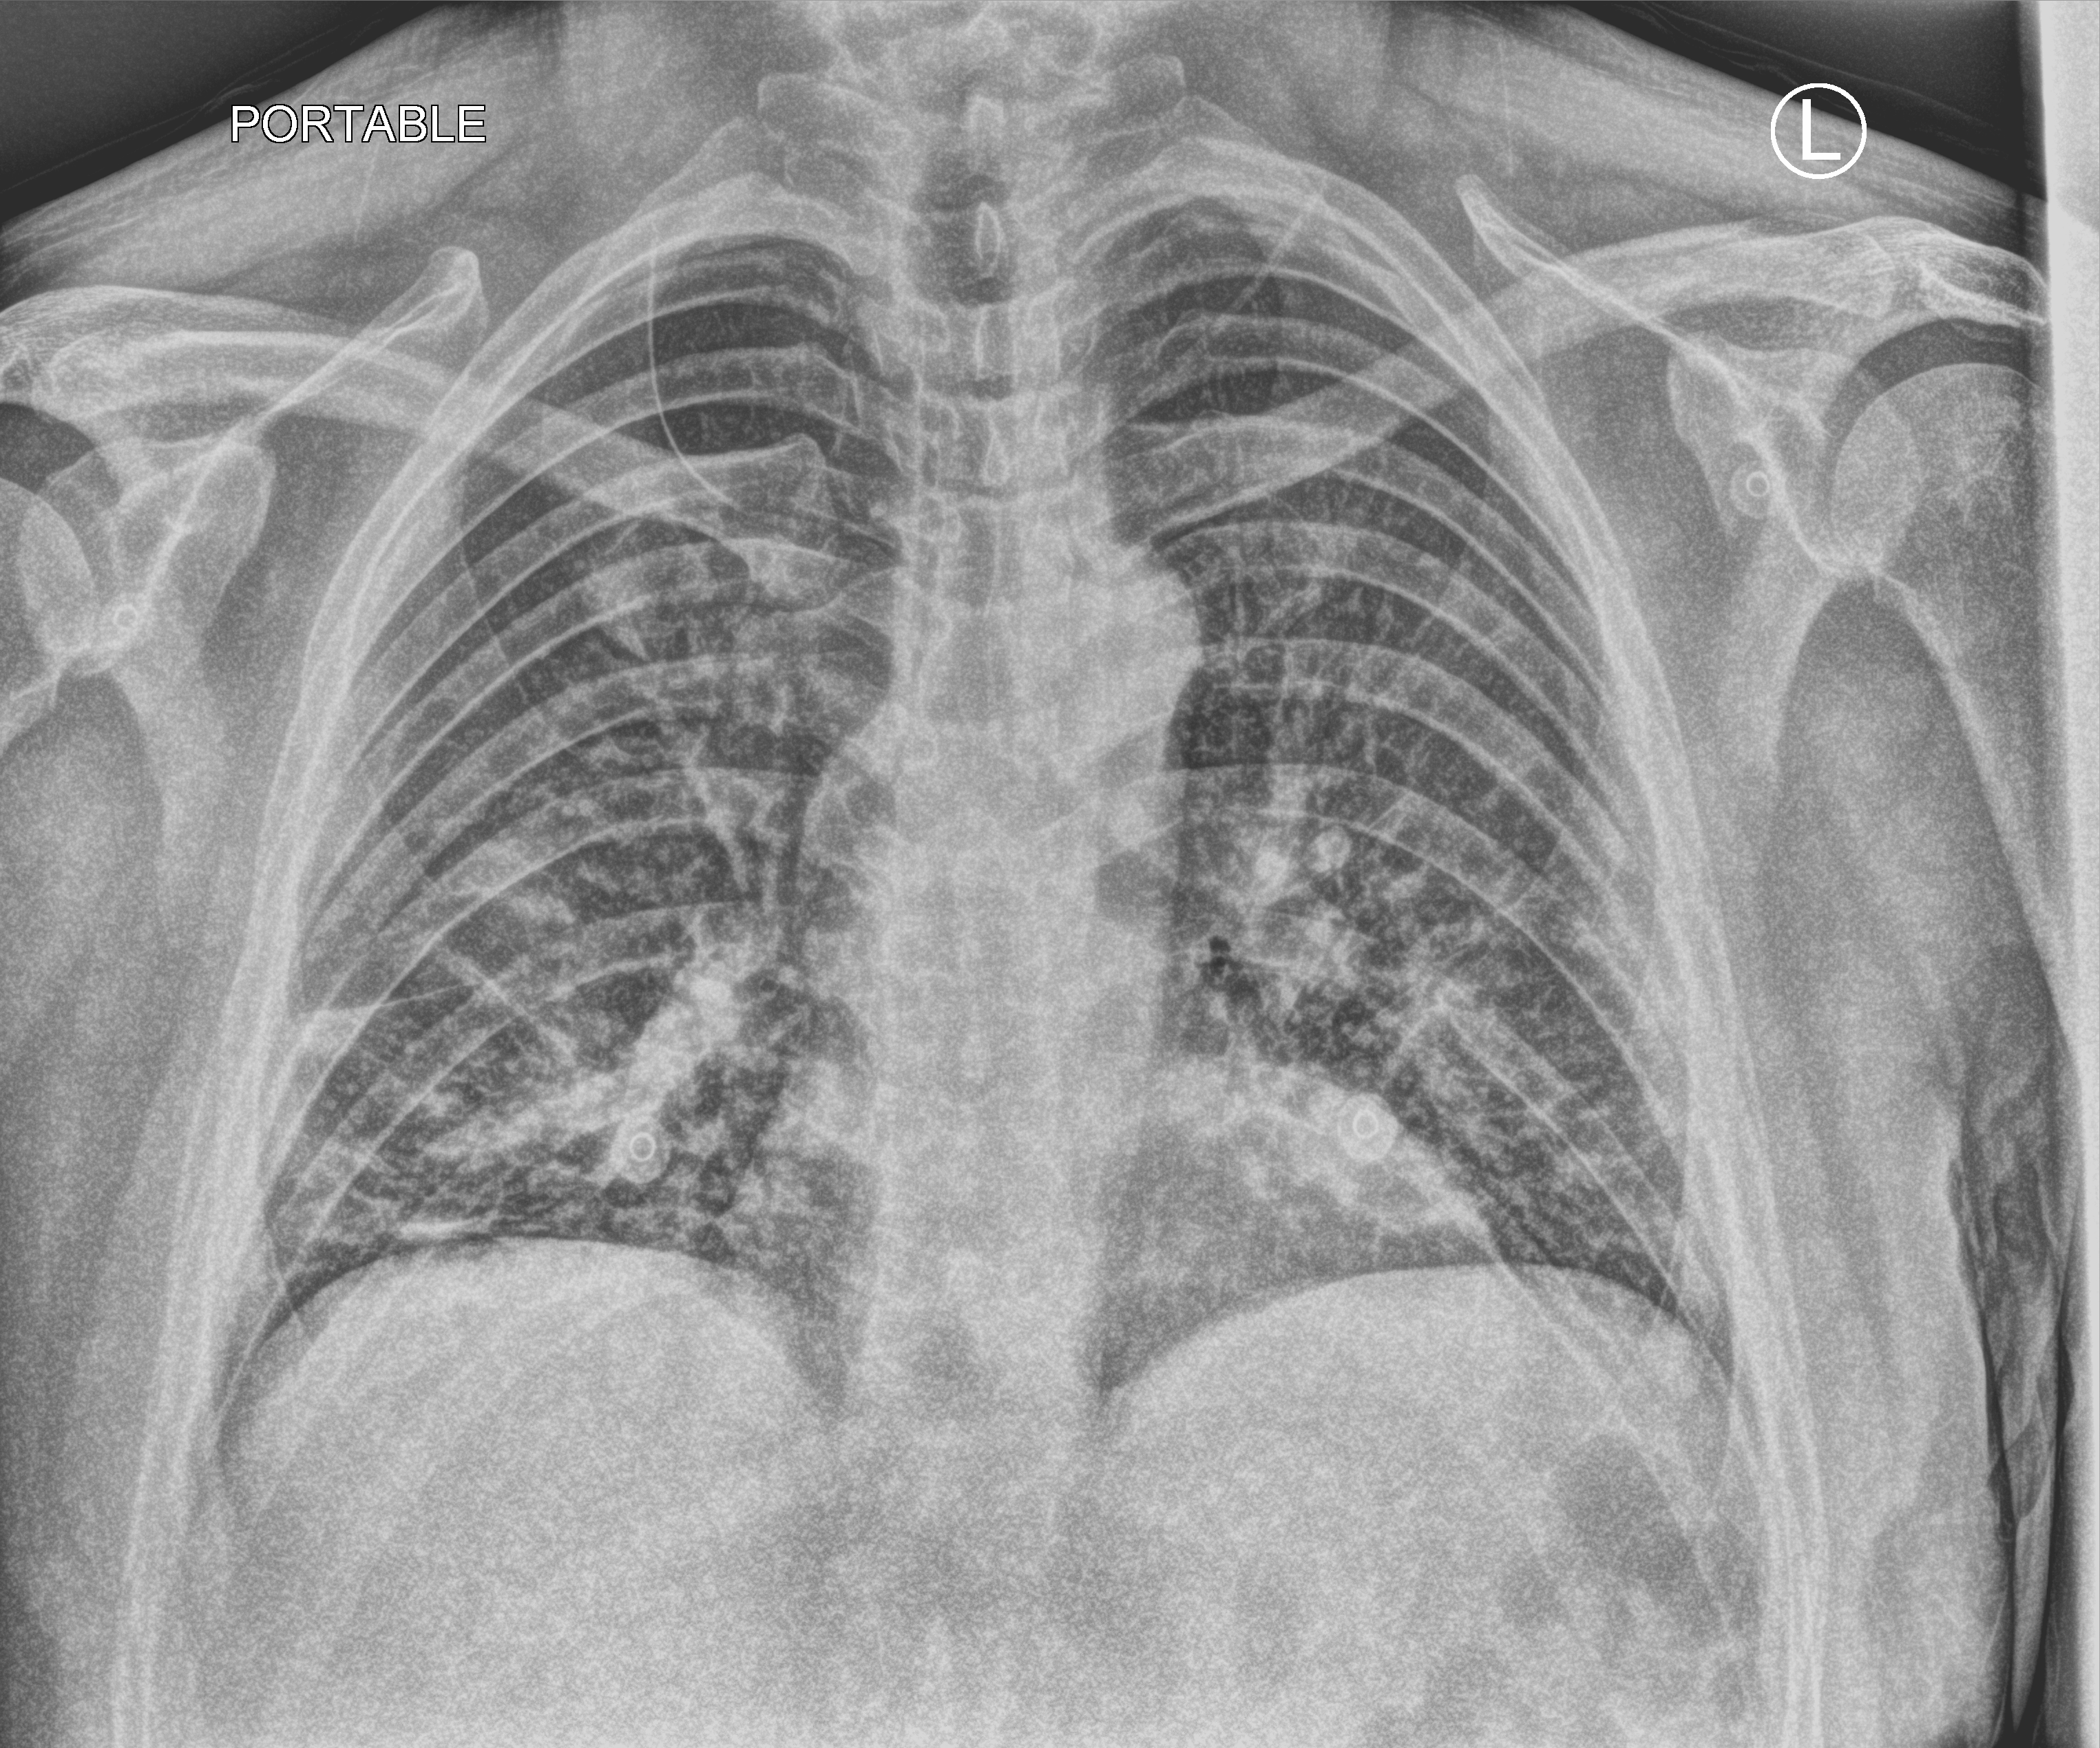
Portable chest radiograph, anteroposterior (AP) projection. Patient hospitalised with COVID-19; male, aged 18–59 years.
Admission-level facts for this patient (not findings on this image; timing relative to this image not recorded): mechanically ventilated during this hospital stay: no.